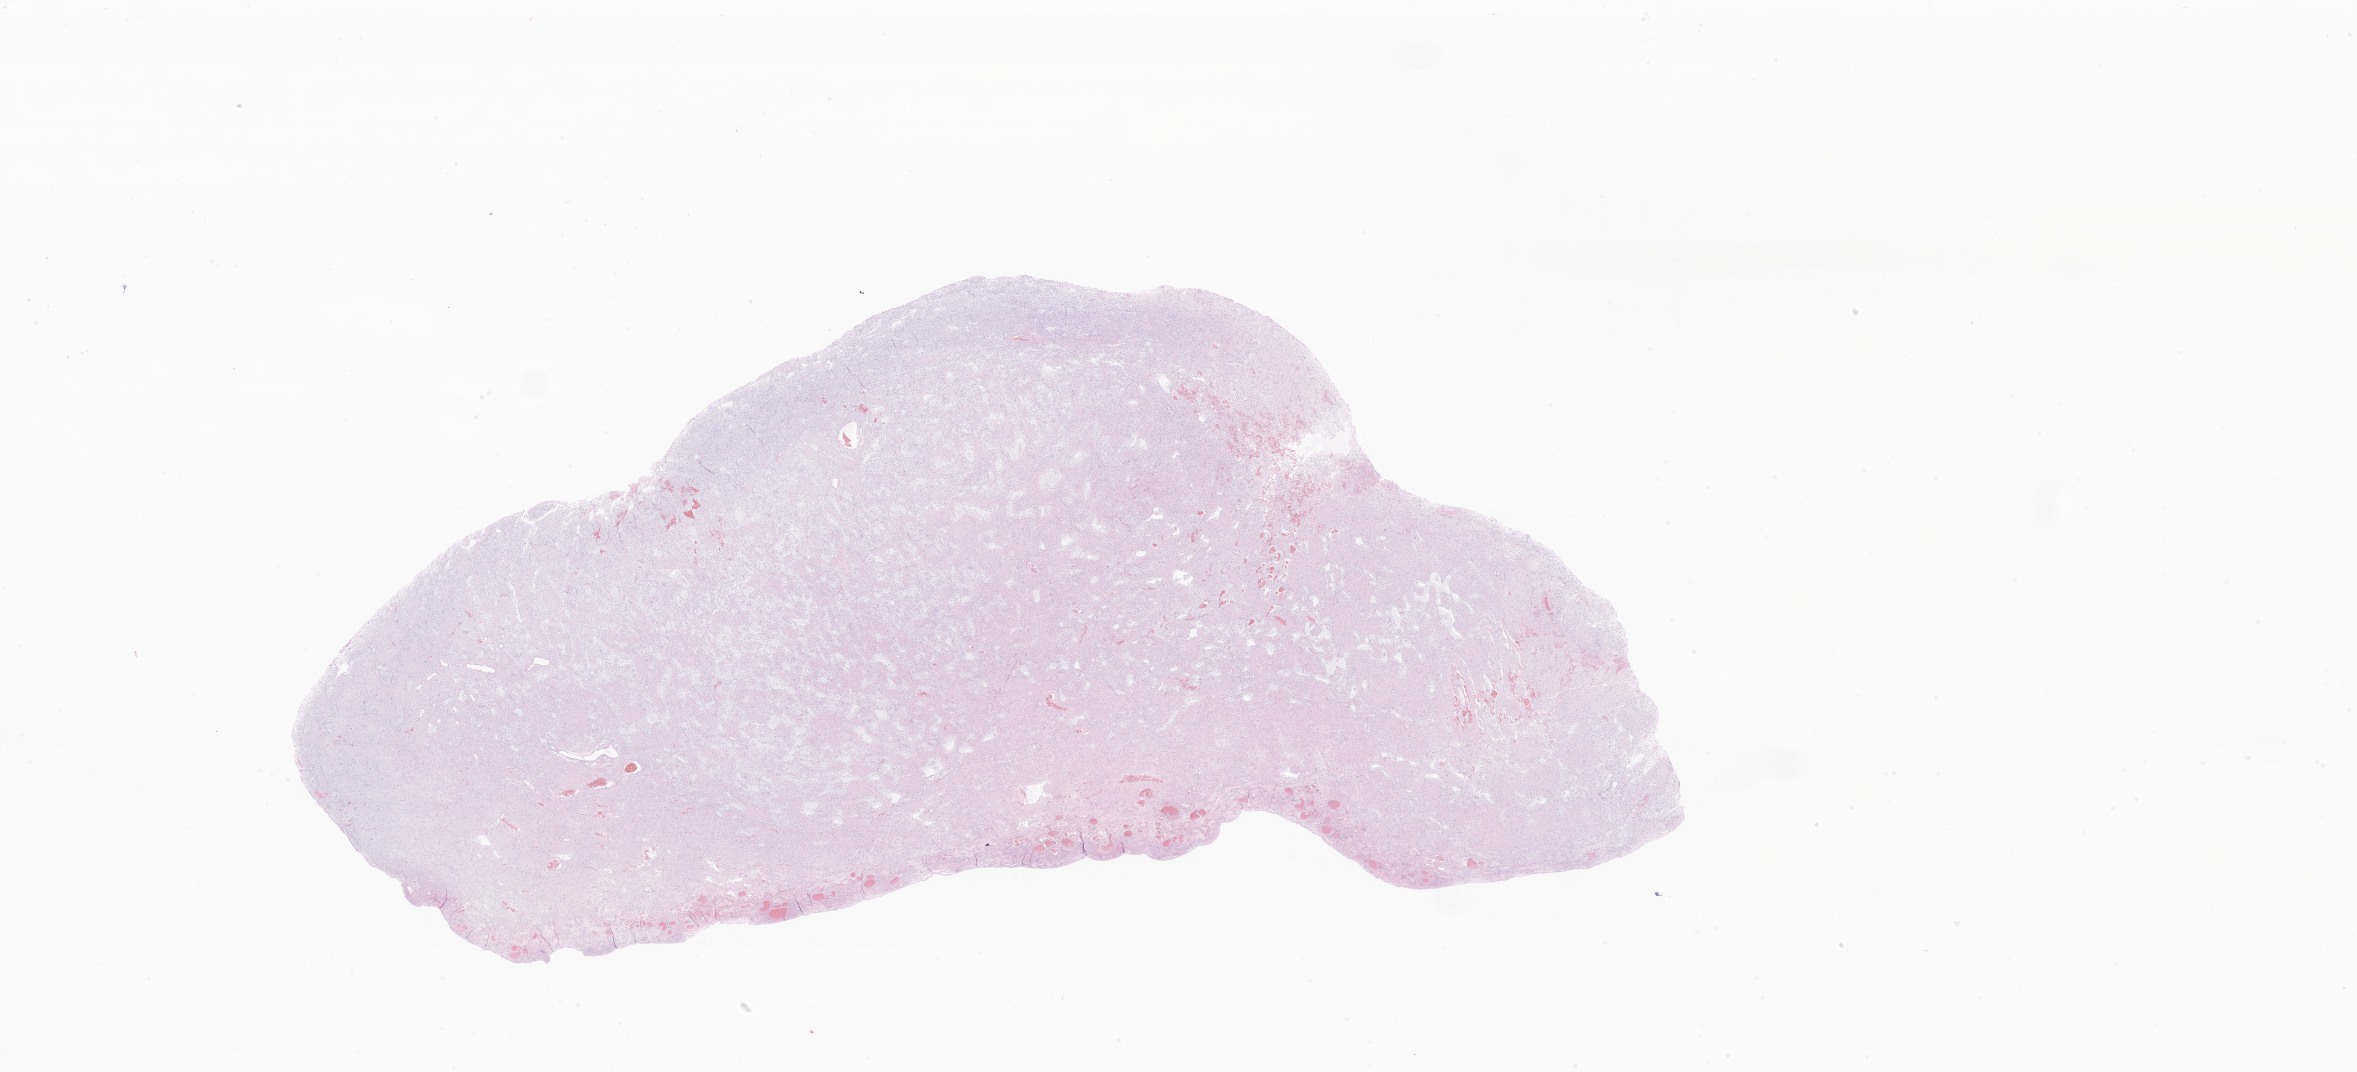
Digitized haematoxylin and eosin-stained section of tumor tissue from the brain — low-resolution overview of the scanned area, about 39.8 x 18.1 mm, FFPE section. Female patient, age 165 months (13 years 9 months).
* diagnosis (ICD-O-3 morphology term): Neoplasm, malignant